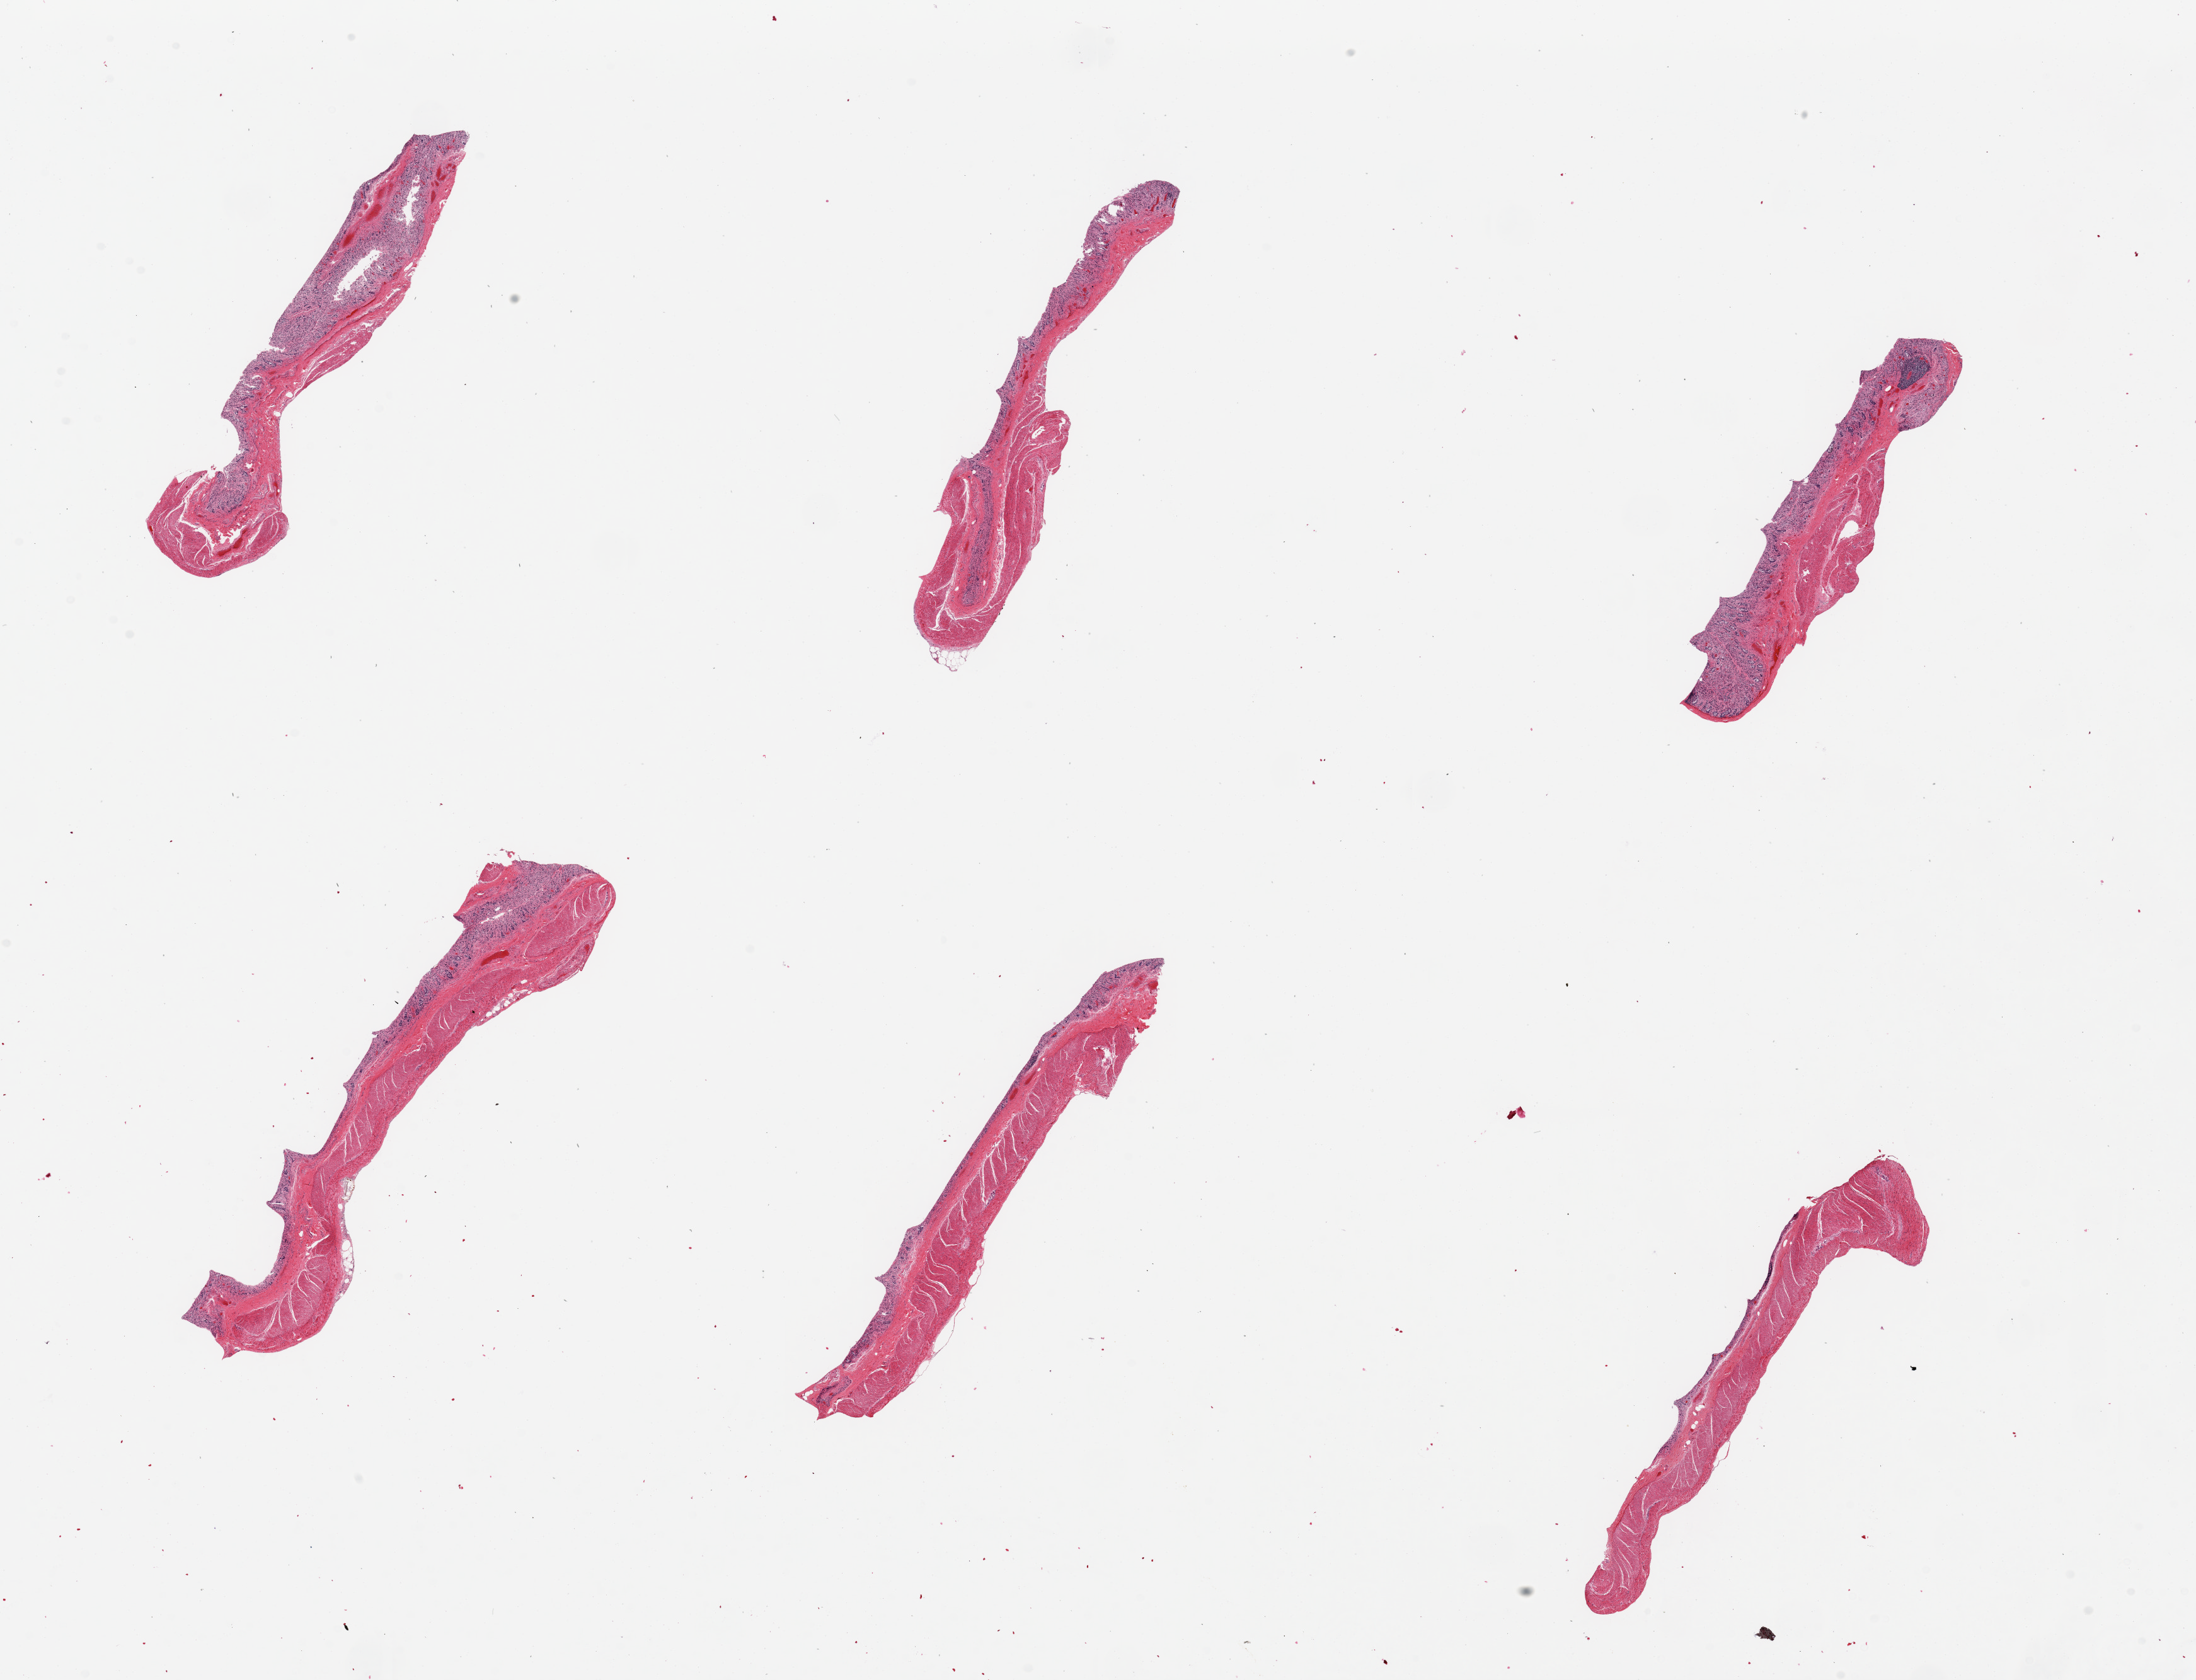
Whole-slide image, H&E stain — low-resolution overview of the scanned area, about 27.6 x 21.1 mm; PAXgene-fixed, paraffin-embedded tissue; sampled site (target tissue): transverse colon; donor tissue sample. Male donor.
Review note (as recorded): 6 pieces ~8 x 1.5mm Mucosa poorly preserved; where visible ~20% of thickness.